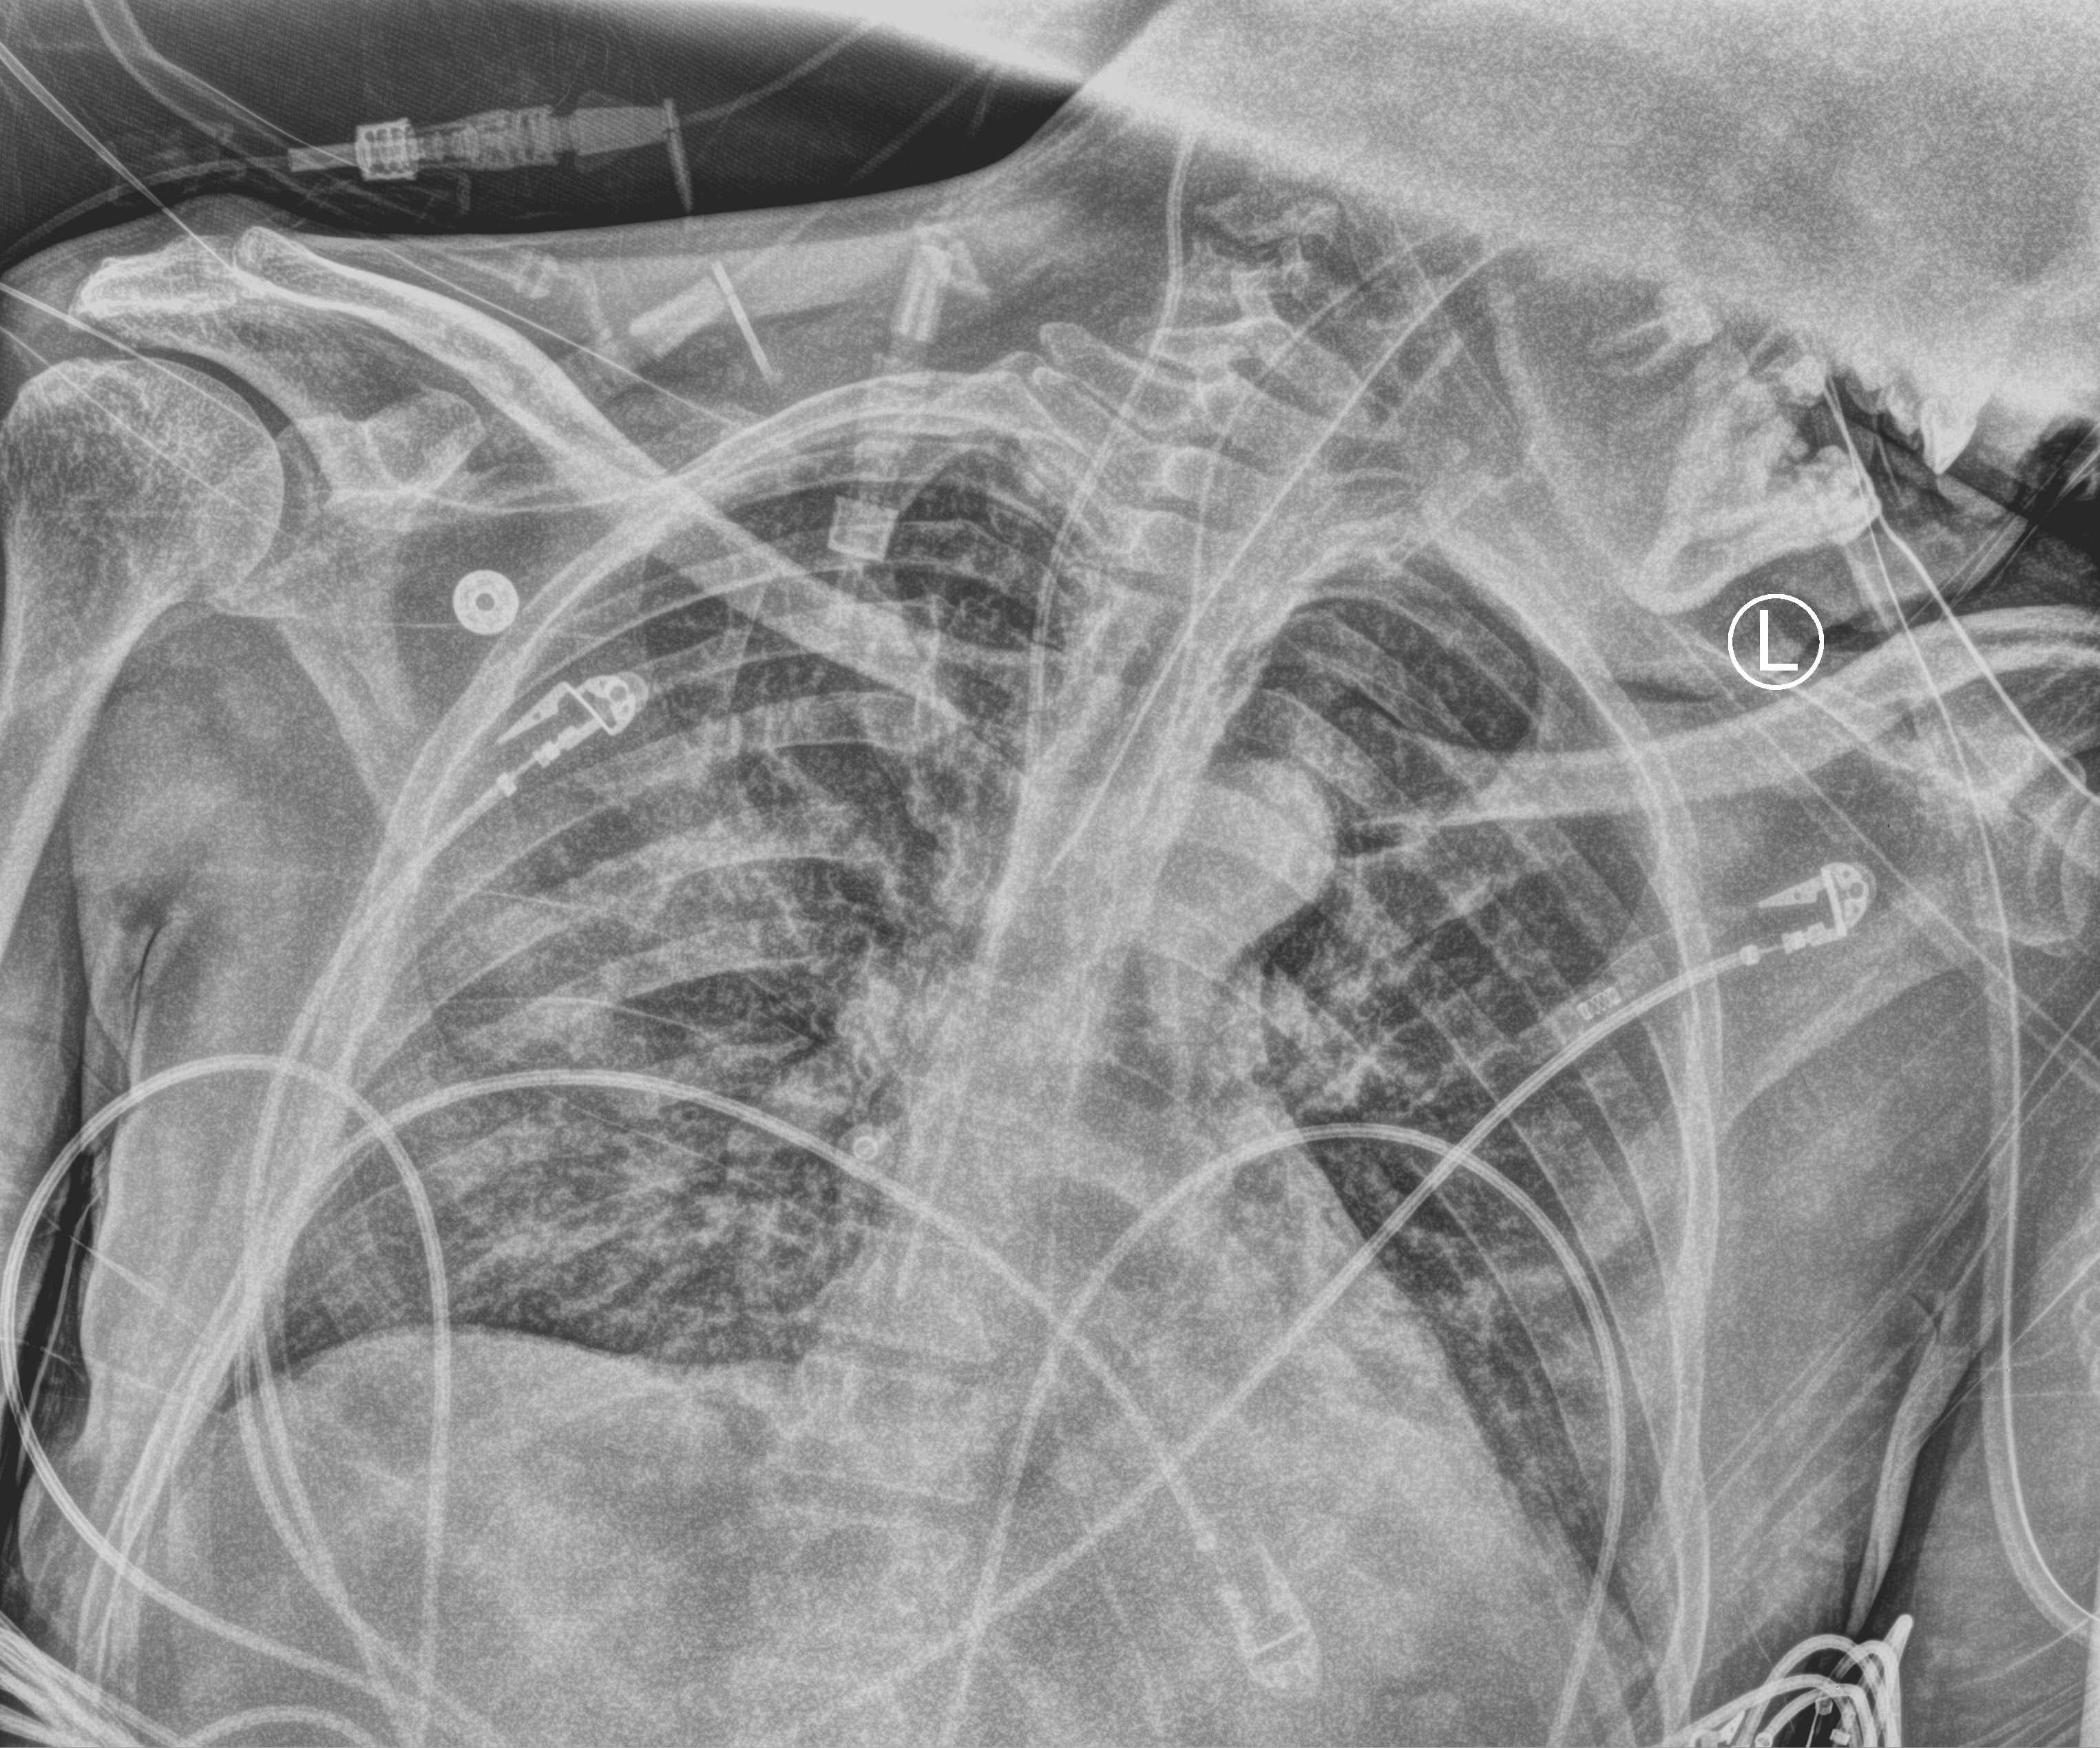
Chest X-ray (portable); anteroposterior (AP) projection. Male patient hospitalised with COVID-19, age 18–59 years.
Hospital-stay facts (about this admission, not read from this image; timing relative to this image not recorded):
- admitted to intensive care during this hospital stay: yes
- diabetes (admission record): yes